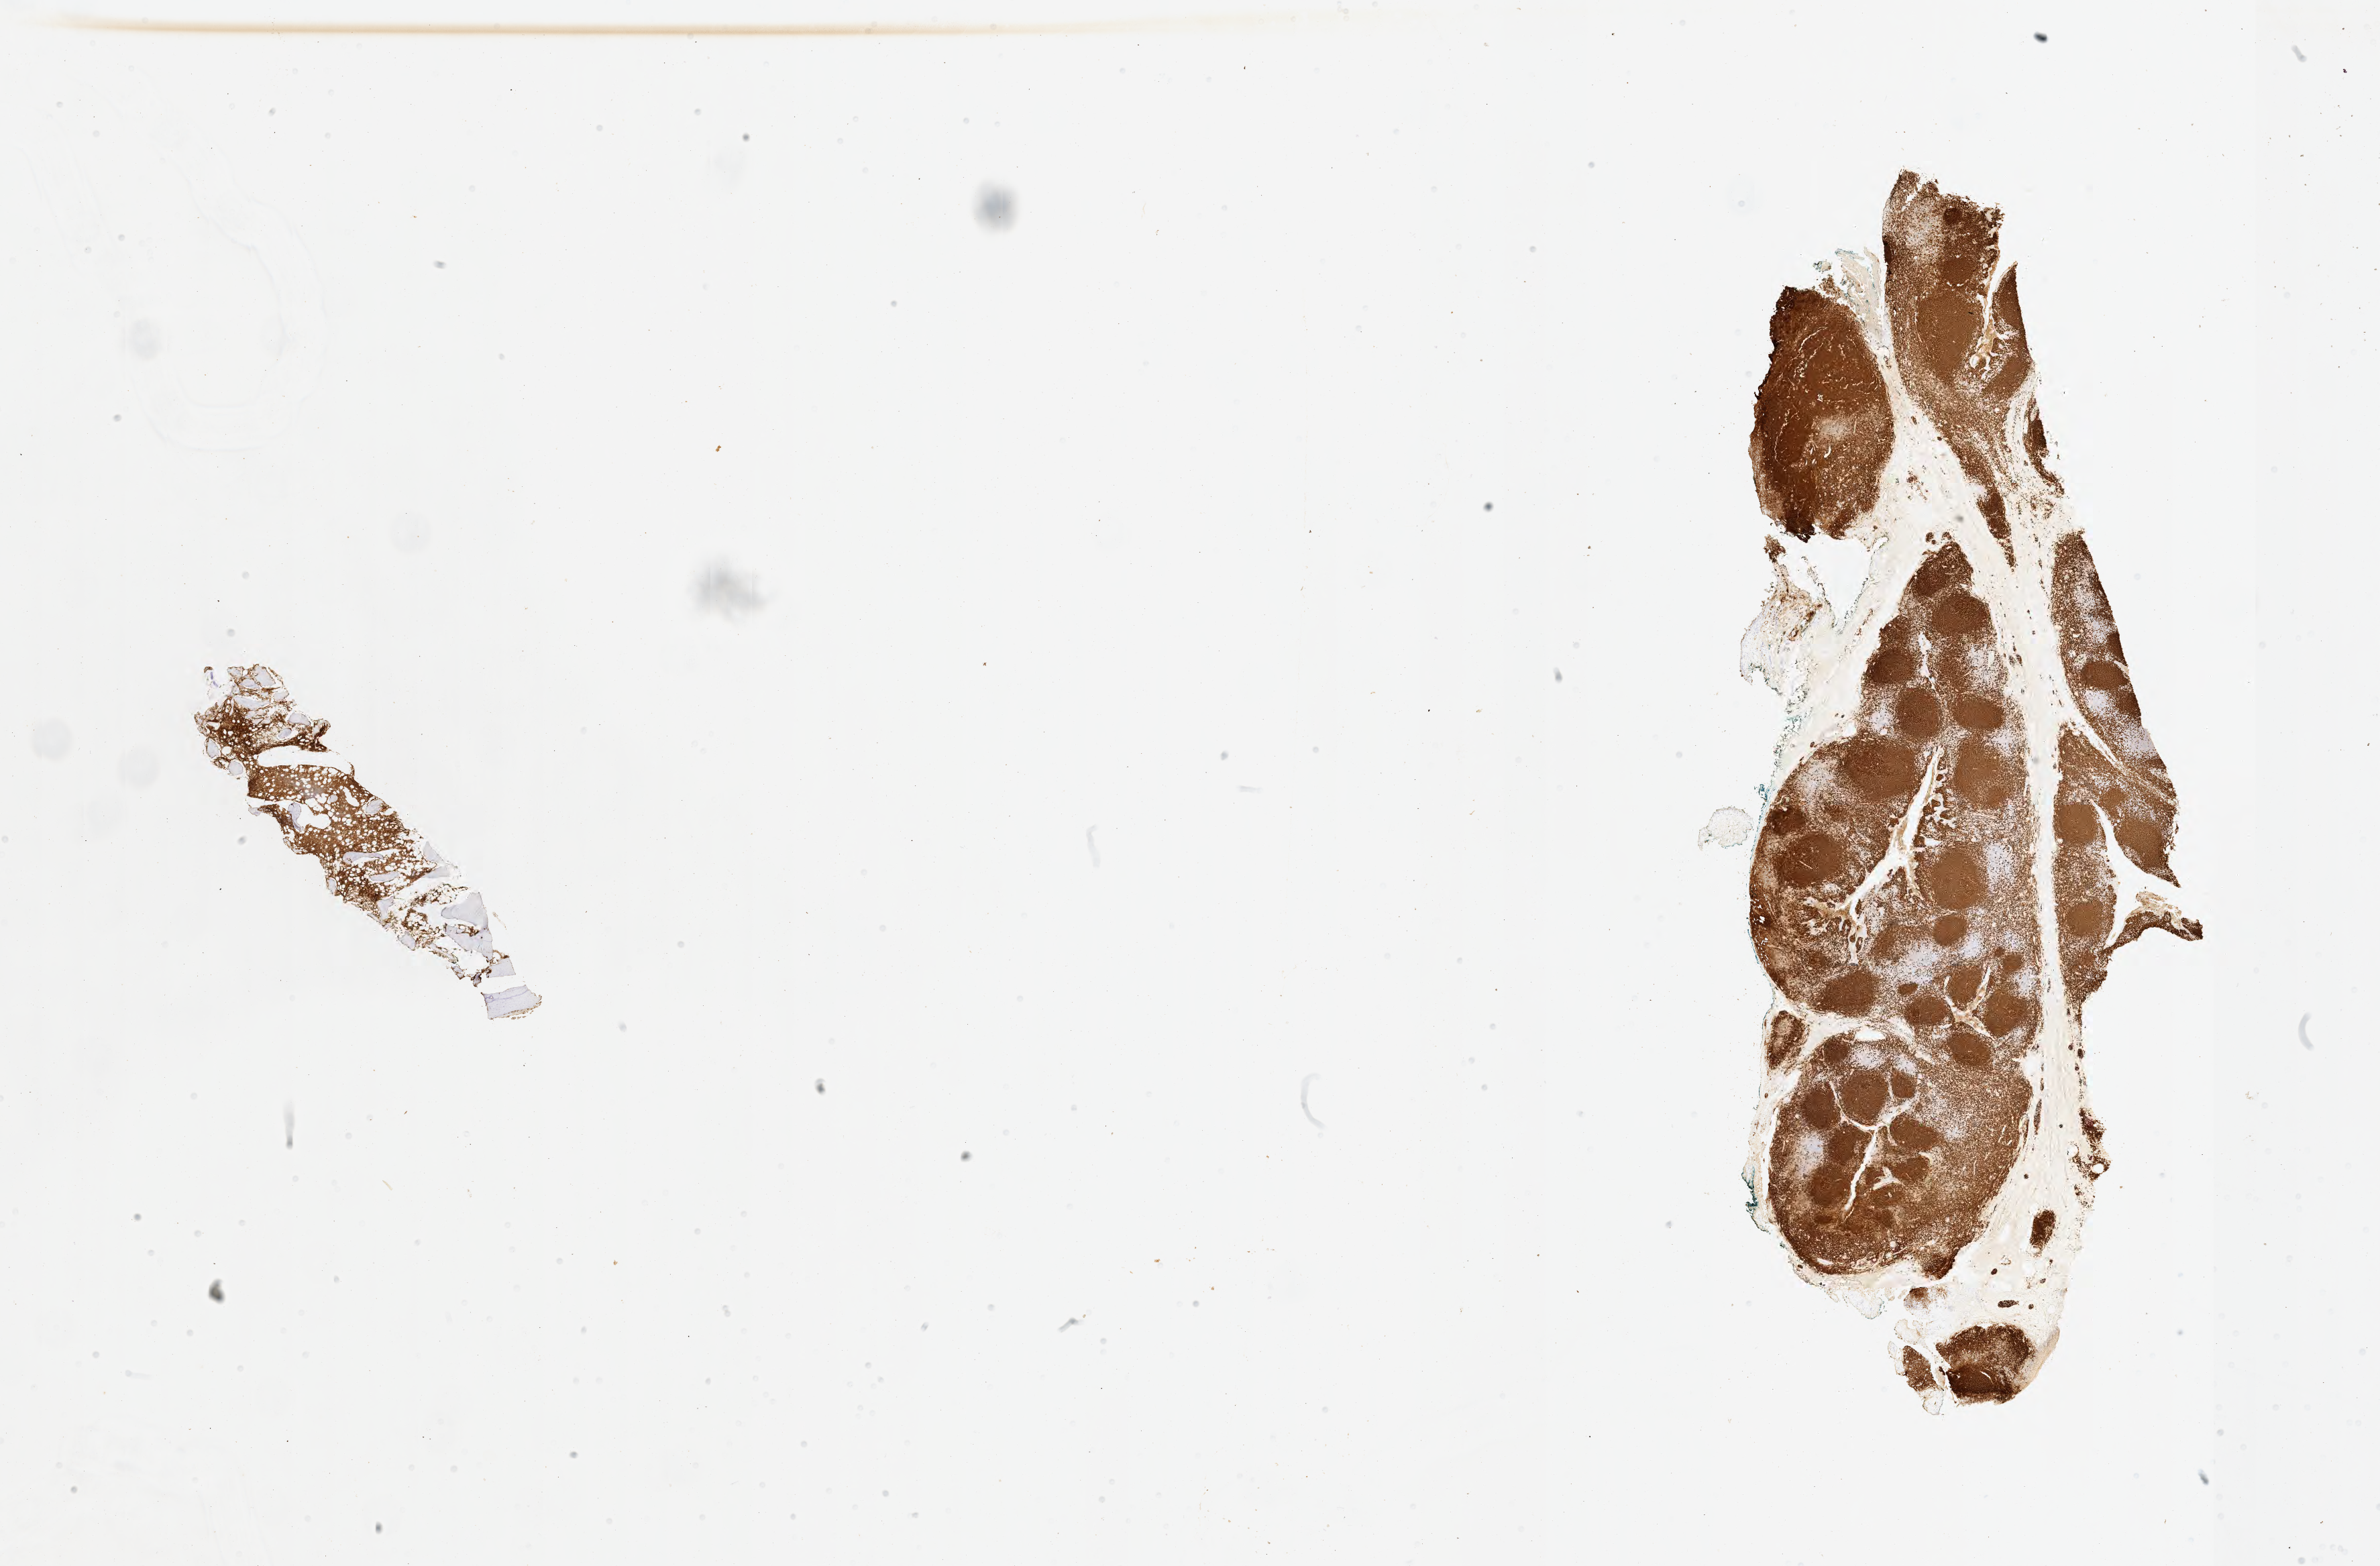
Whole-slide image, immunohistochemical stain for CD20, whole scanned area (about 28.7 x 18.9 mm) shown as a low-resolution overview. Tumor tissue. Site: bone marrow. Patient: female, age at initial diagnosis 4 years.
Diagnosis: Burkitt lymphoma, NOS.